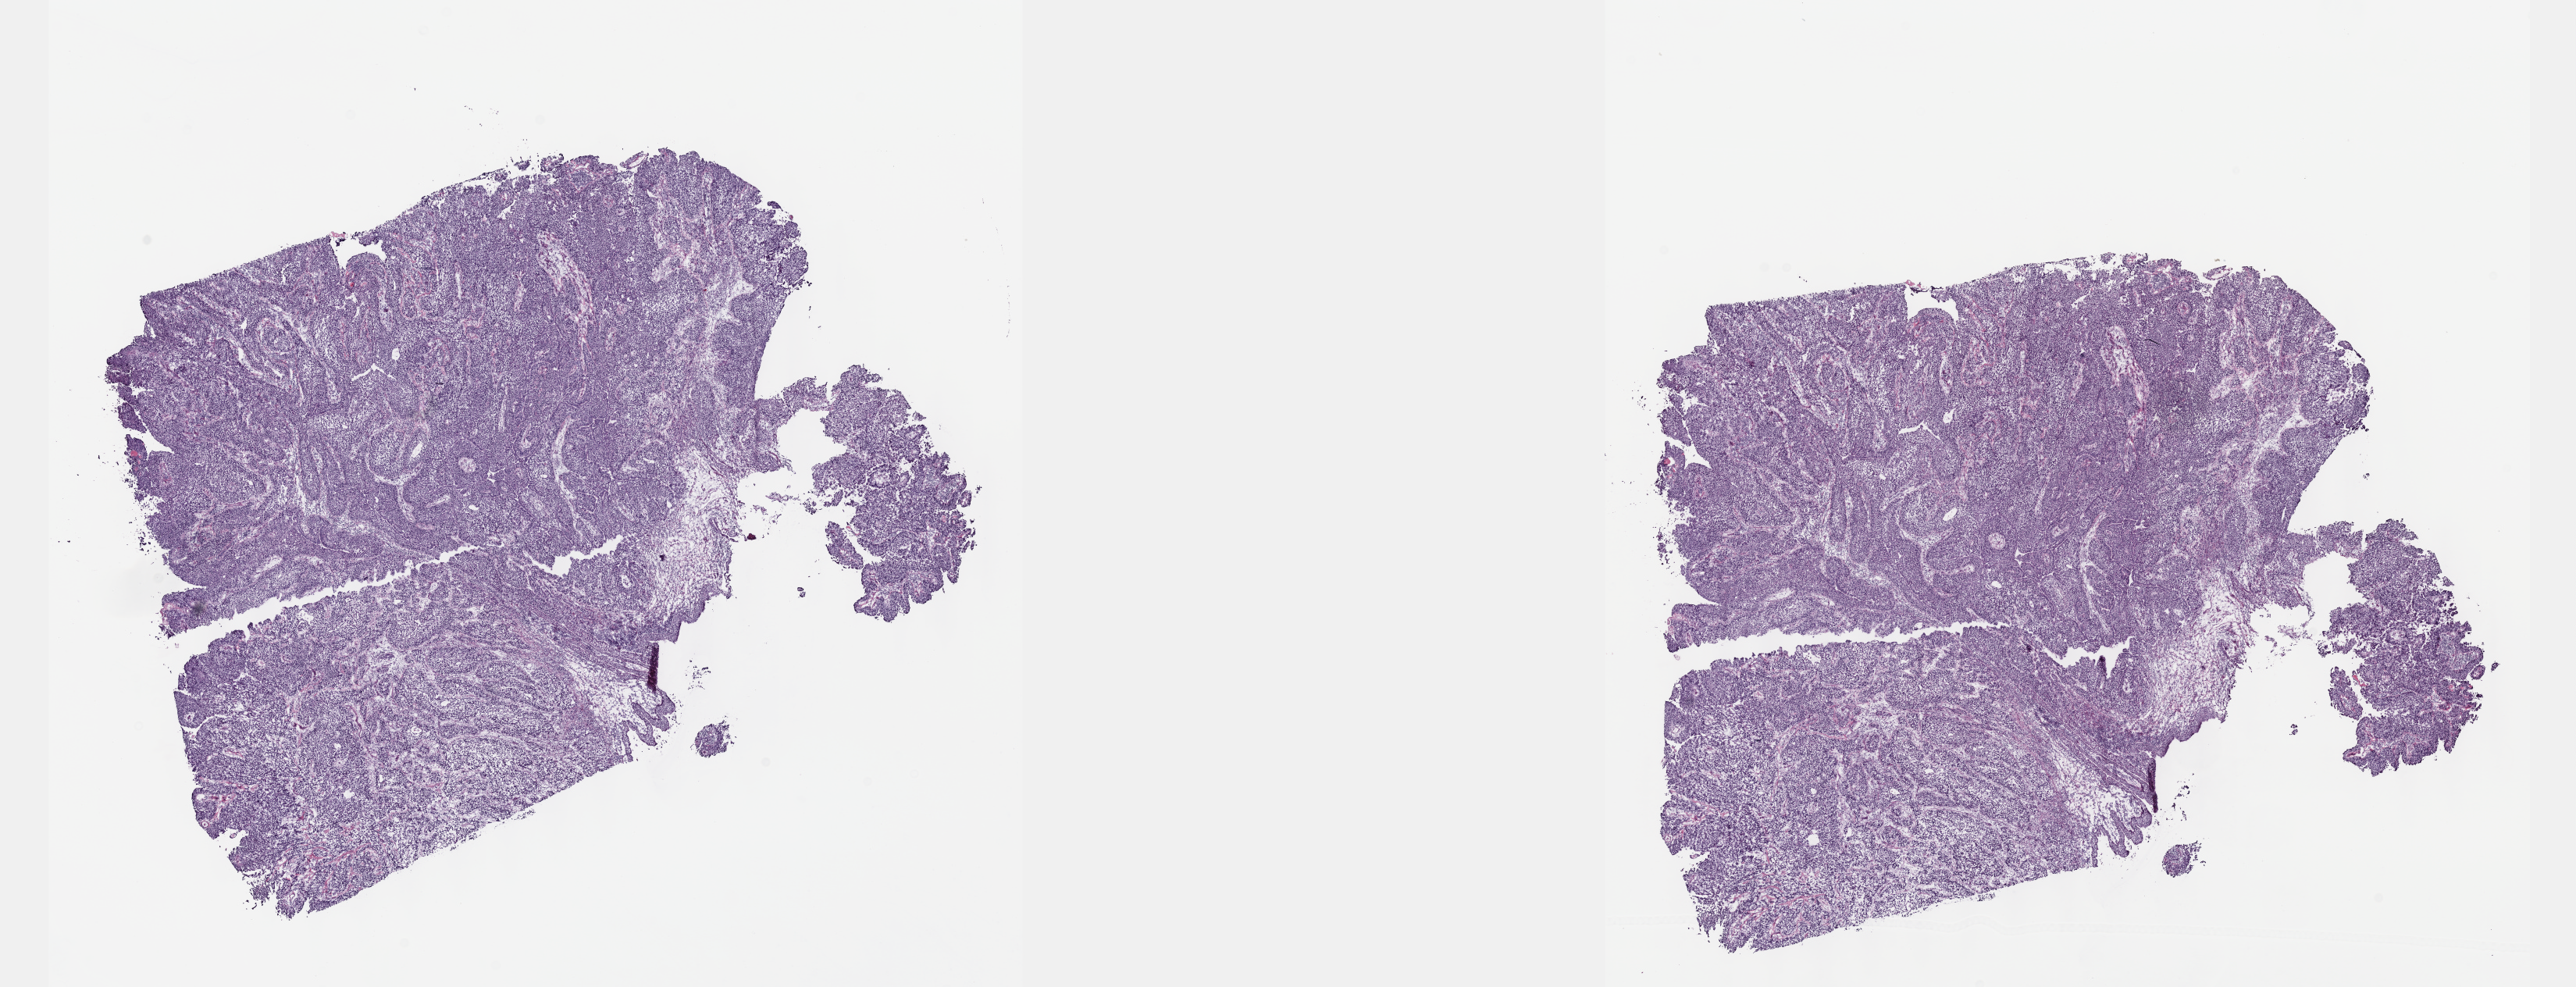
Digitized H&E-stained tissue section (whole slide), whole scanned area (about 26.7 x 10.2 mm) shown as a low-resolution overview; frozen section; sample: primary tumour, bladder. Female patient; age at initial diagnosis 59 years. Histologic grade: high grade. Composition of this section per pathologist review: tumour cells 100%, tumour nuclei 80%, normal cells 0%, stromal cells 0%, necrosis 0%. Inflammatory infiltration, as recorded: lymphocyte infiltration 3%, monocyte infiltration 0%, neutrophil infiltration 0%.
- AJCC pathologic stage: II (6th edition)
- lymph nodes positive (case pathology): 0 of 67 examined
- histologic diagnosis: Papillary transitional cell carcinoma (lateral wall of bladder)